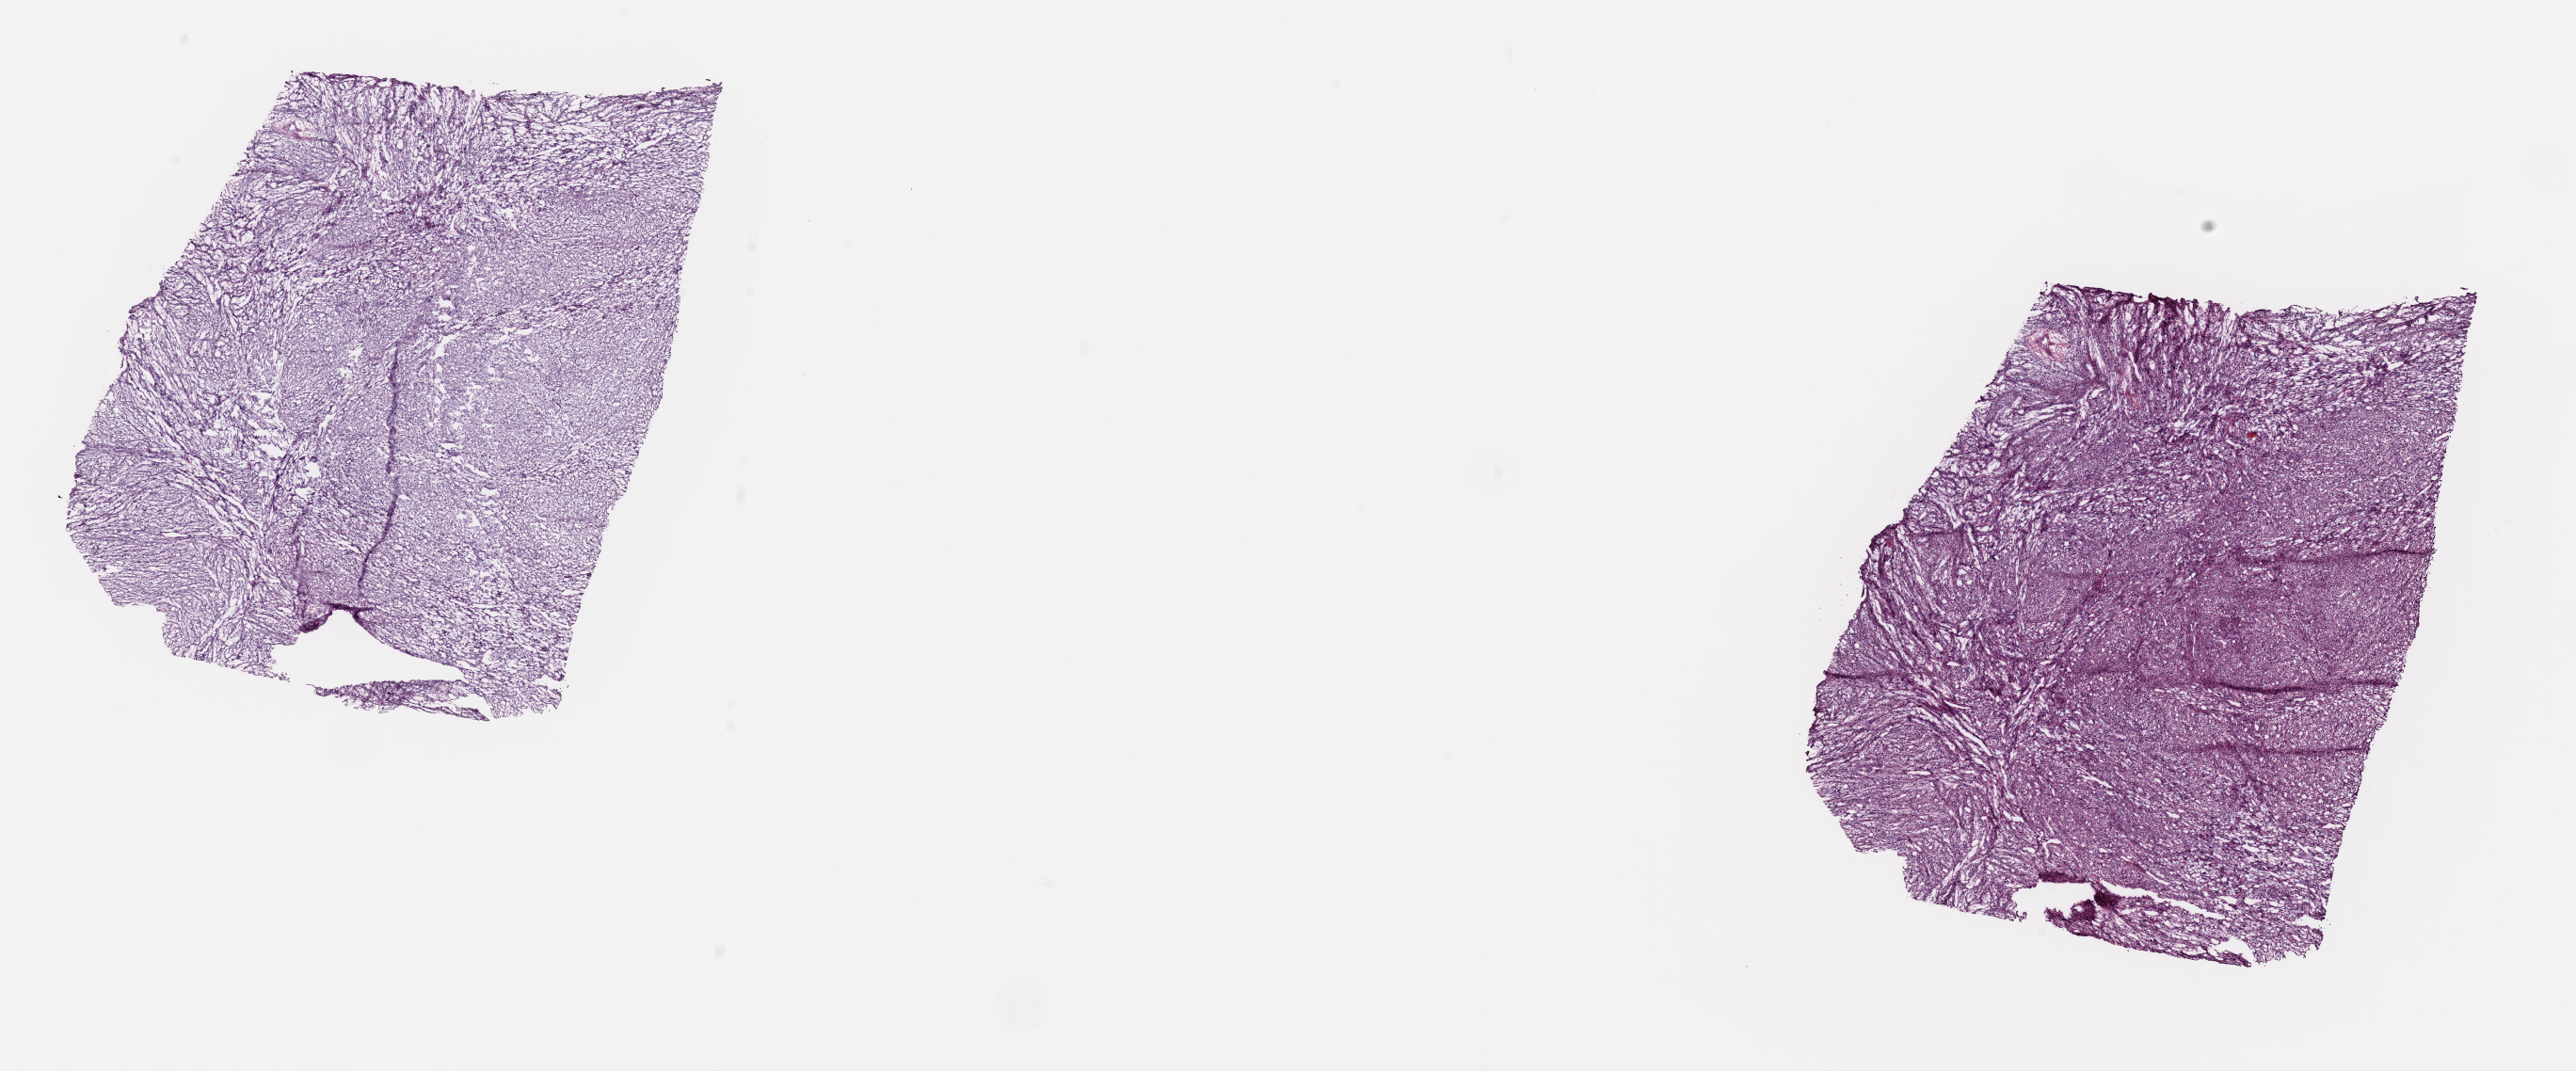
Digitized Hematoxylin and eosin (H&E) stained tissue section (whole slide), shown as a low-resolution overview of the whole scanned area (about 21.6 x 9.0 mm). Frozen section from the top of the tissue portion. Retroperitoneum and peritoneum, primary tumour sample. Male patient; age at initial diagnosis 61 years.
Histologic diagnosis: Dedifferentiated liposarcoma (retroperitoneum).